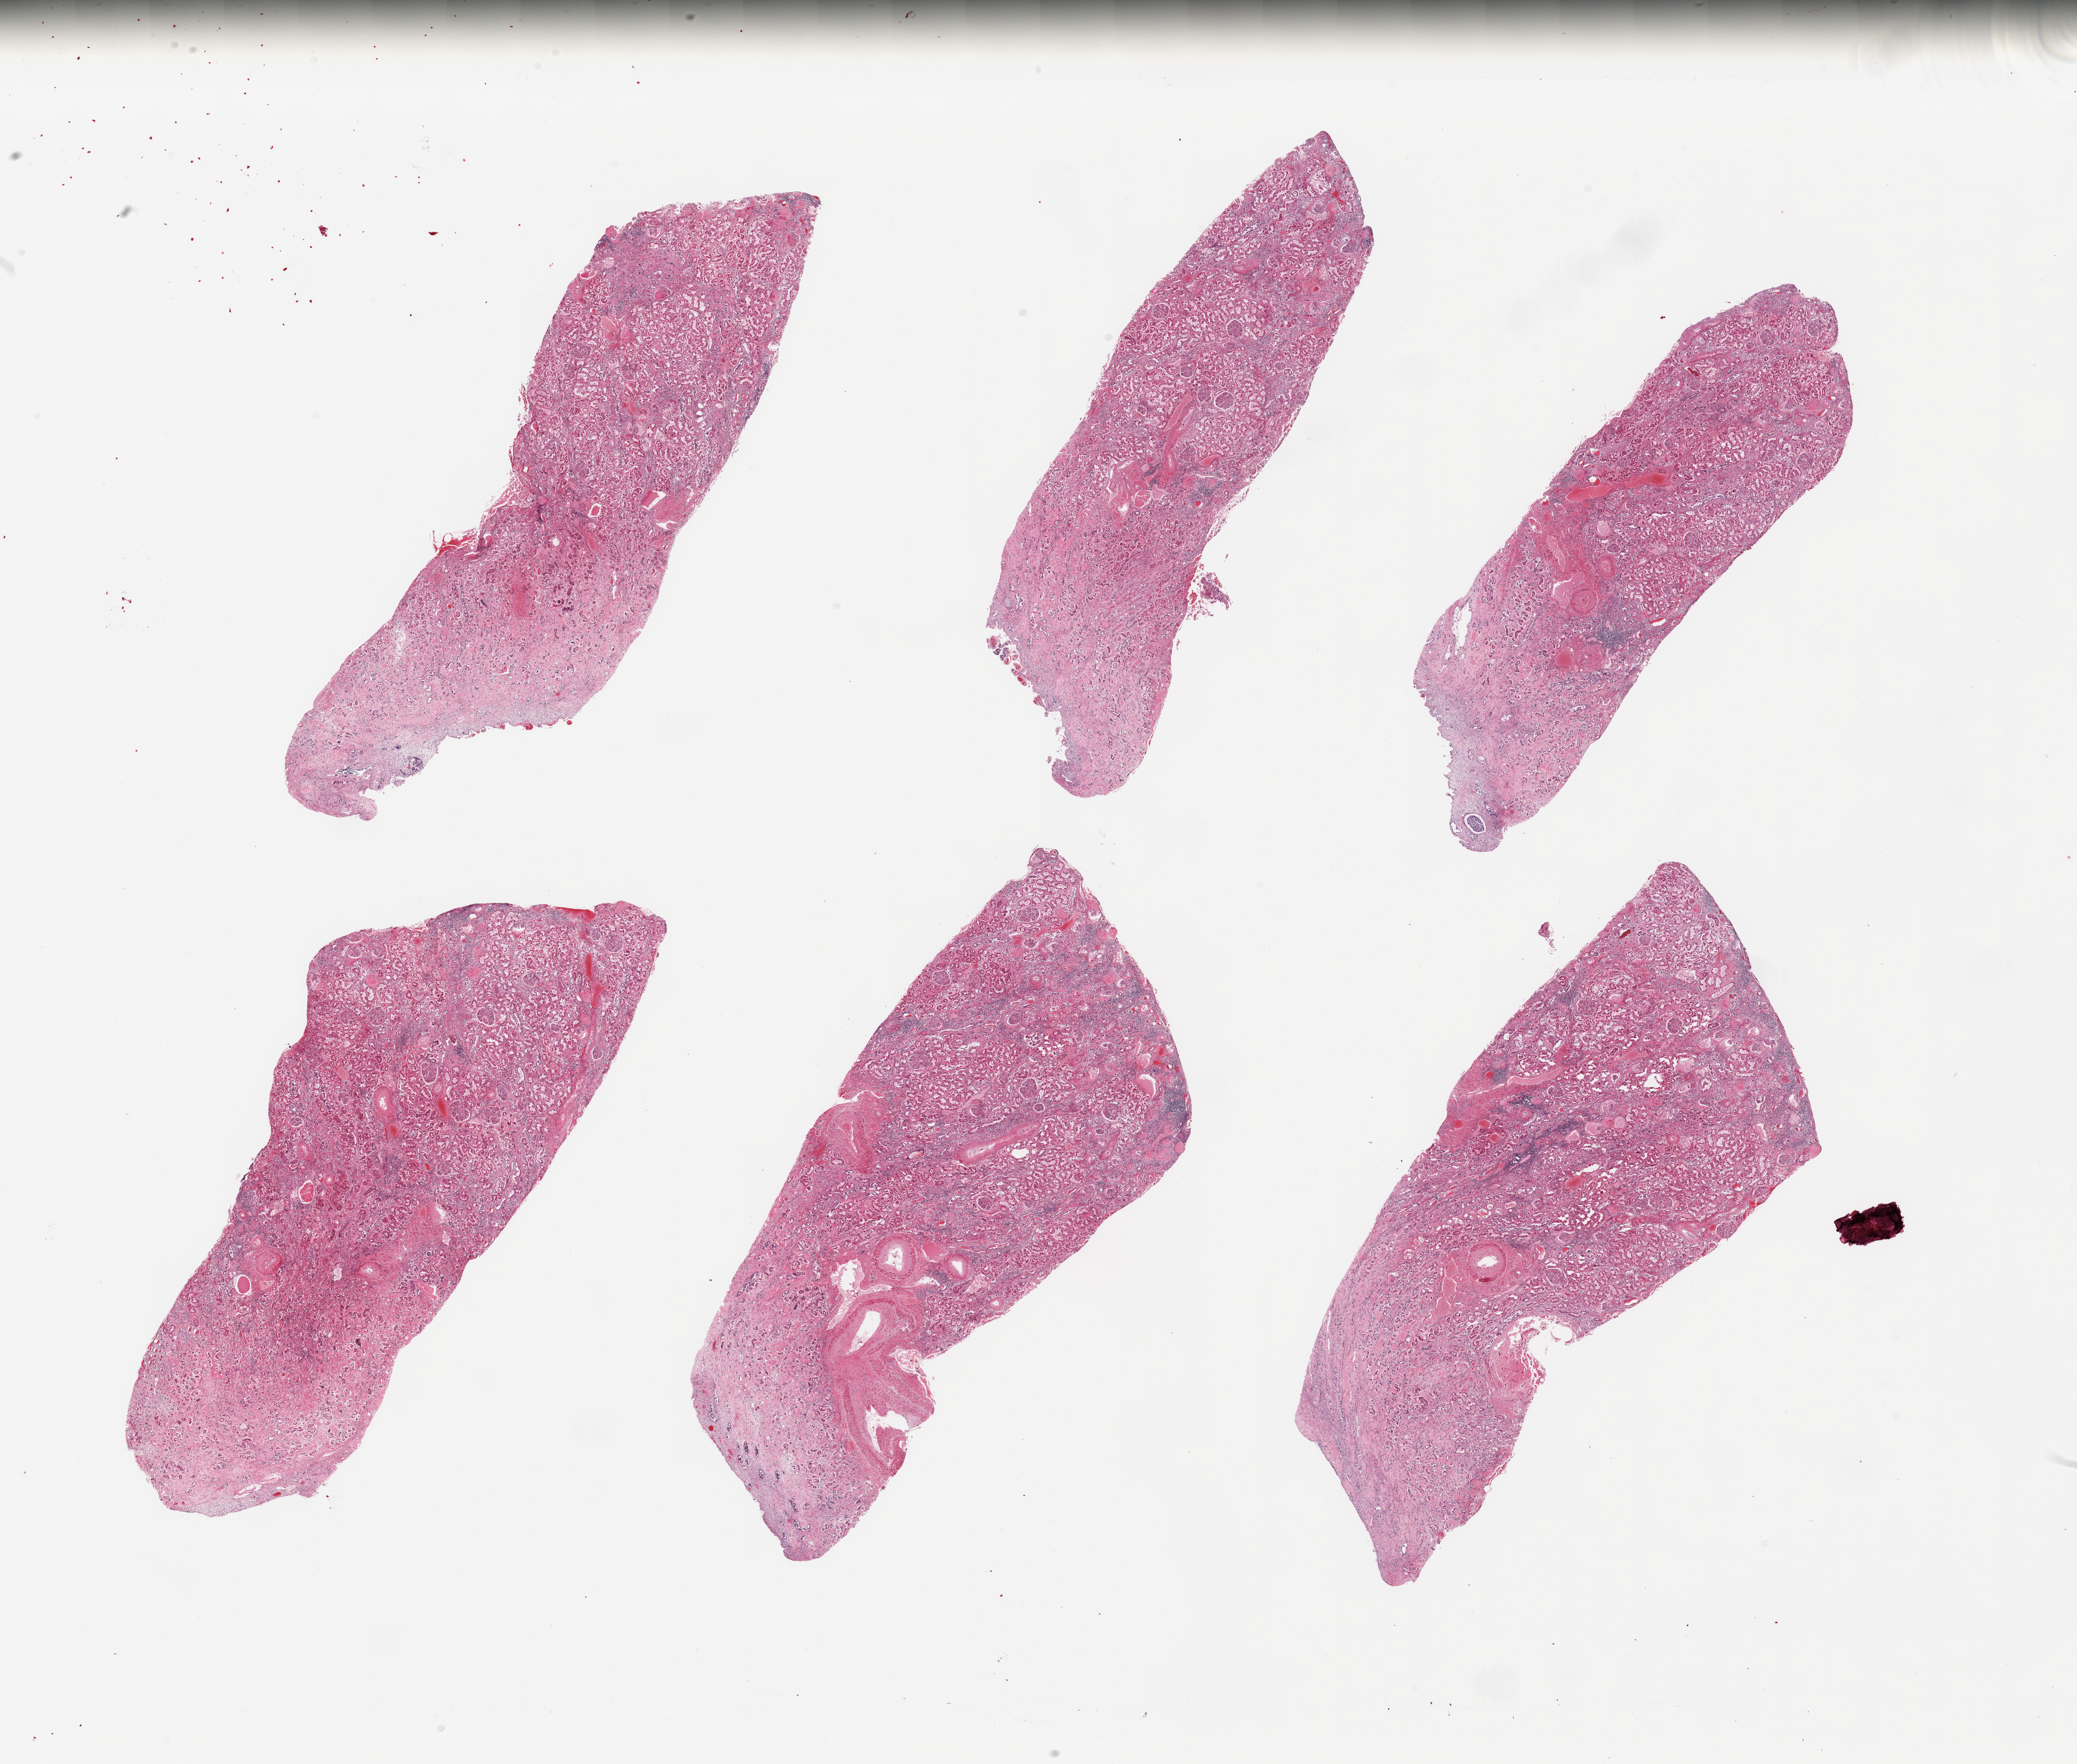
Digitized haematoxylin and eosin-stained section, brightfield — low-resolution overview of the scanned area, about 27.6 x 23.4 mm (from a 20x scan), PAXgene-fixed paraffin-embedded (PFPE) section, sampled site (target tissue): renal cortex, donor tissue sample. Male donor.
• review note (as recorded): 6 pieces; all include portion of medulla (not target), arterio and arteriolonephrosclerosis, hyalinized glomeruli, chronic interstitial inflammation